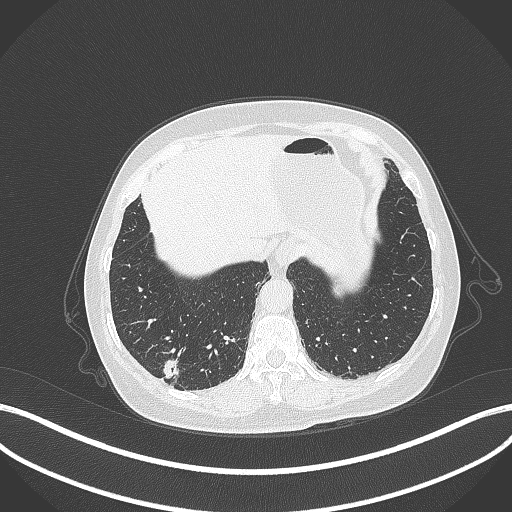
Chest CT, one axial slice. Slice 52 of 333 in the series (ordered by position). 120 kVp. Lung window (W 1500 / L -600 HU). 1 mm slice thickness. 512 × 512 image matrix. Female patient, age 69 years. From the clinical record (not read from this slice): clinical TNM (as recorded): T1b N0 M0; histopathological grade: G2-3.
Structures marked on this image (bounding box drawn by a radiologist):
- lung tumour (recorded histology: adenocarcinoma): bounding box [x1, y1, x2, y2] px = [162, 354, 183, 382]